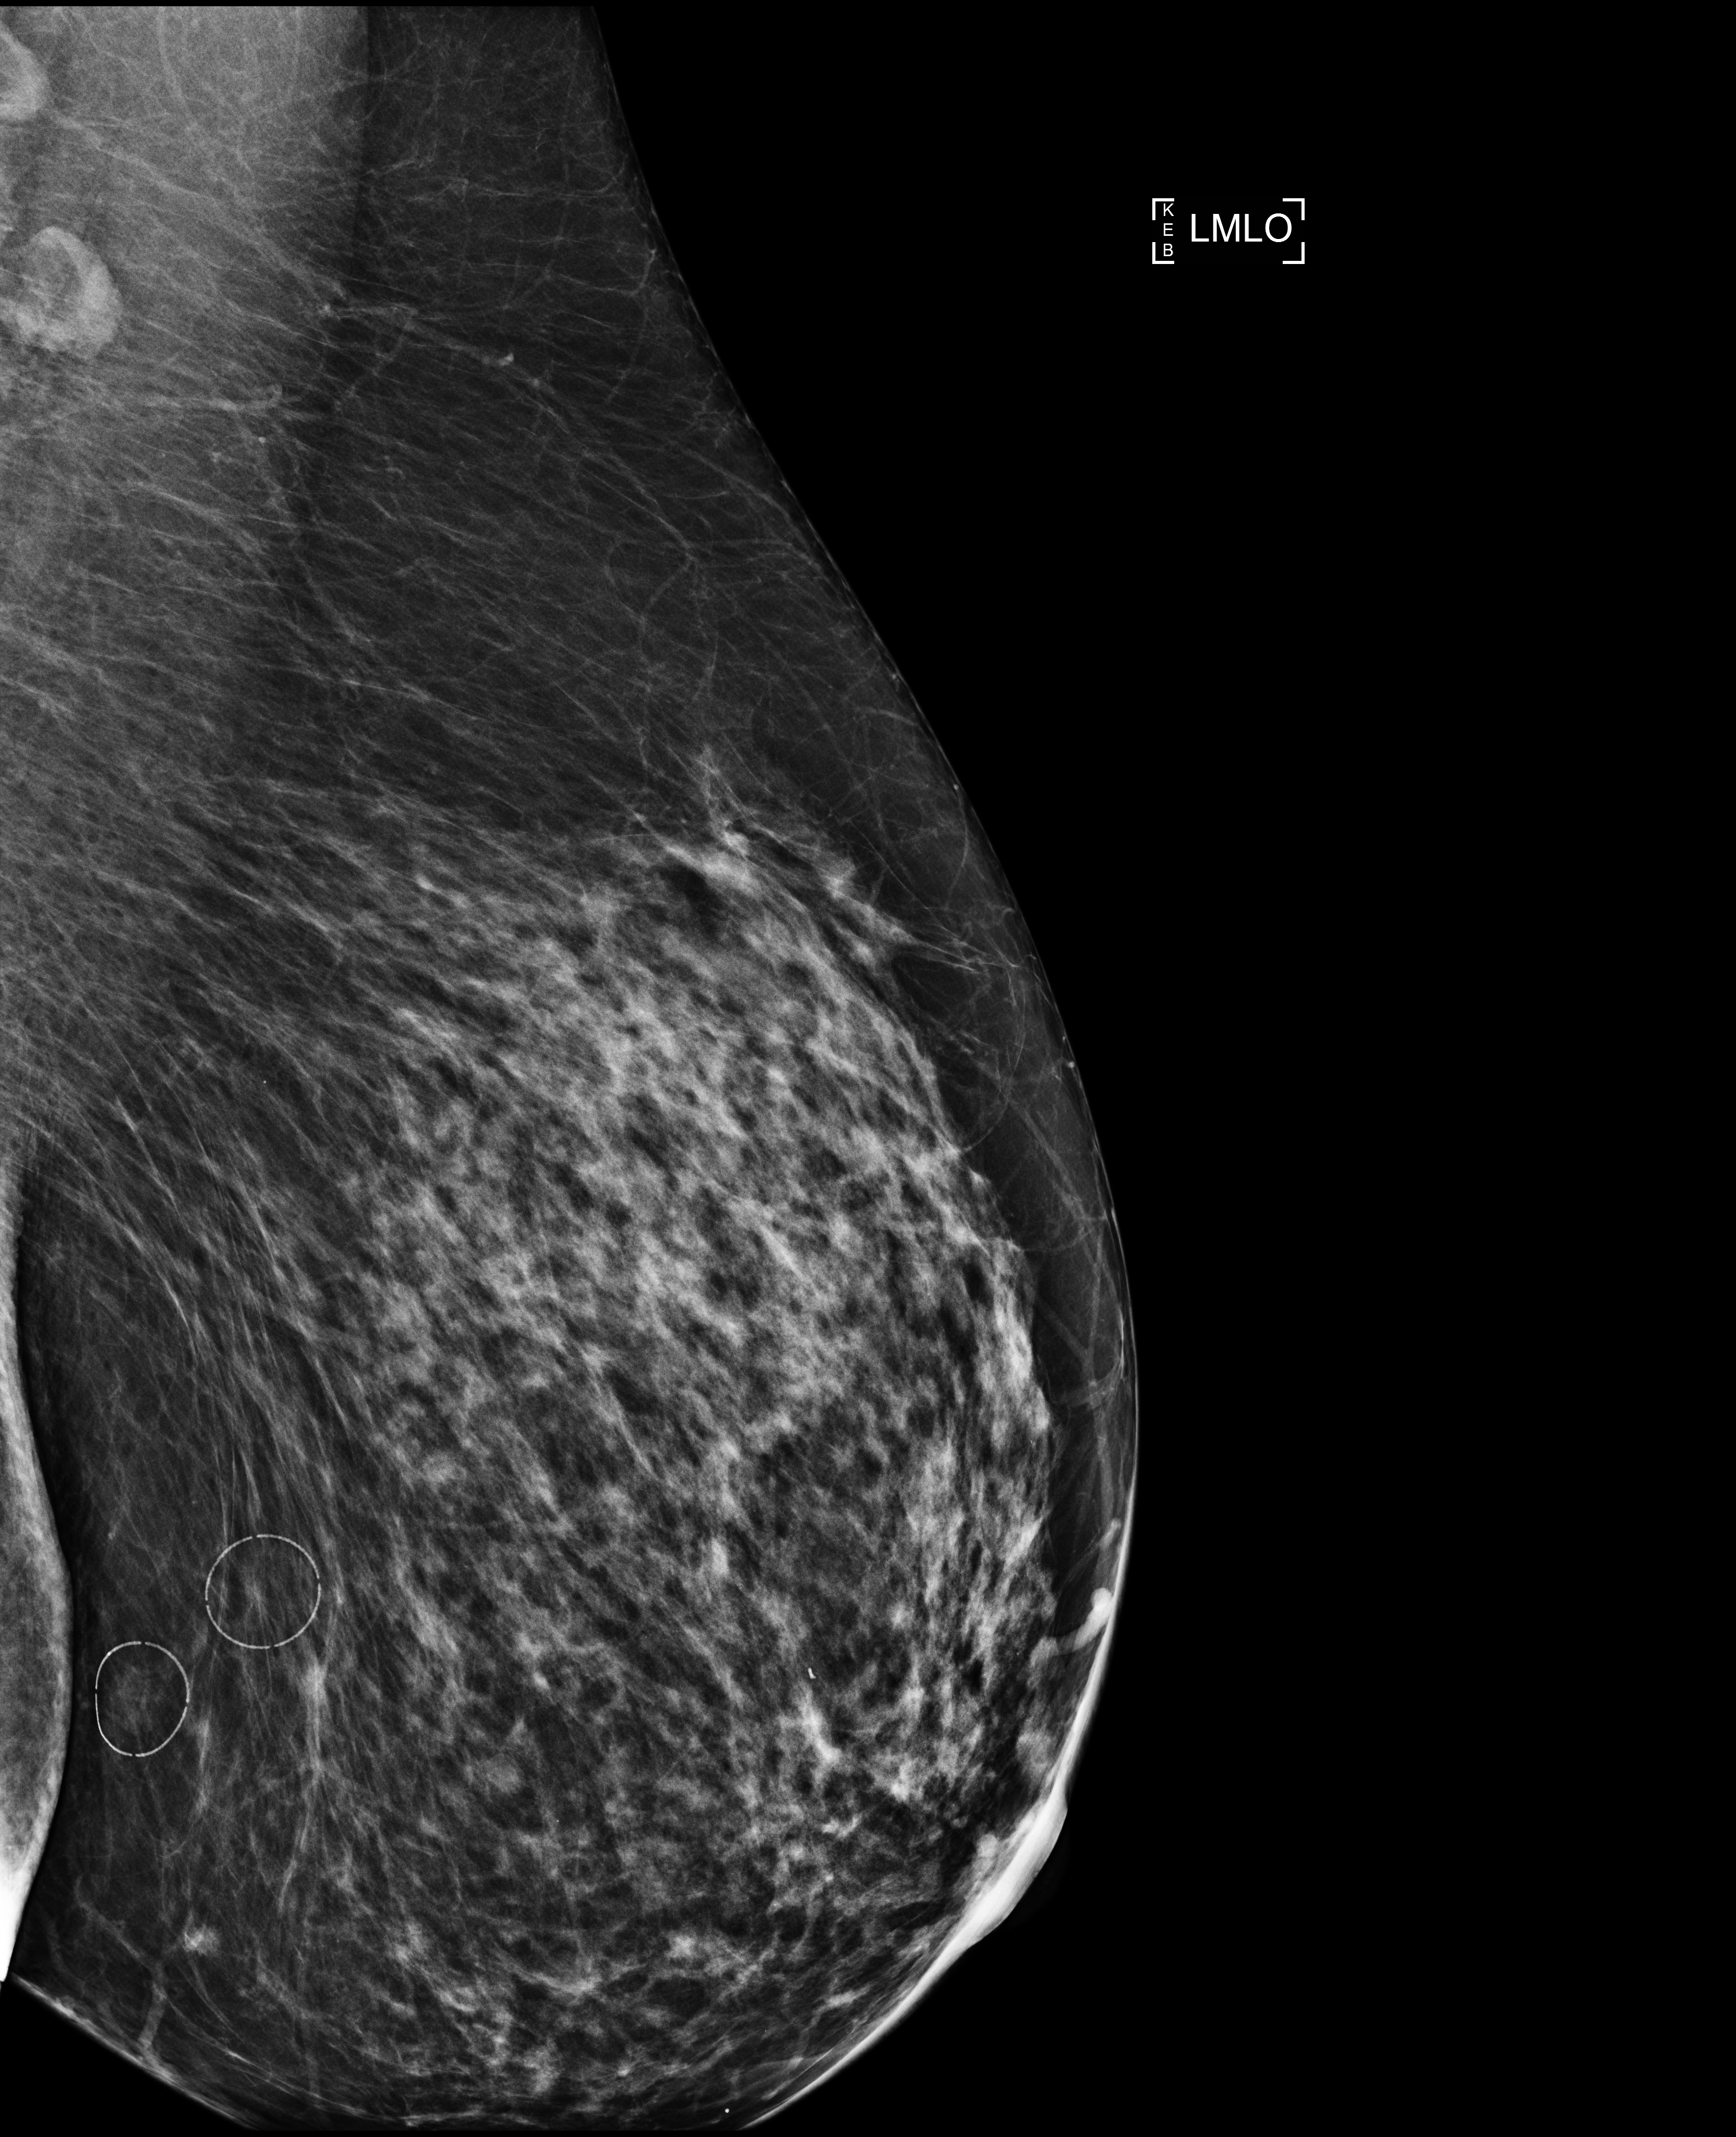
Screening examination. Patient: female, 62 years.
Image type: full-field digital mammogram. Breast: left. Projection: medio-lateral oblique projection.